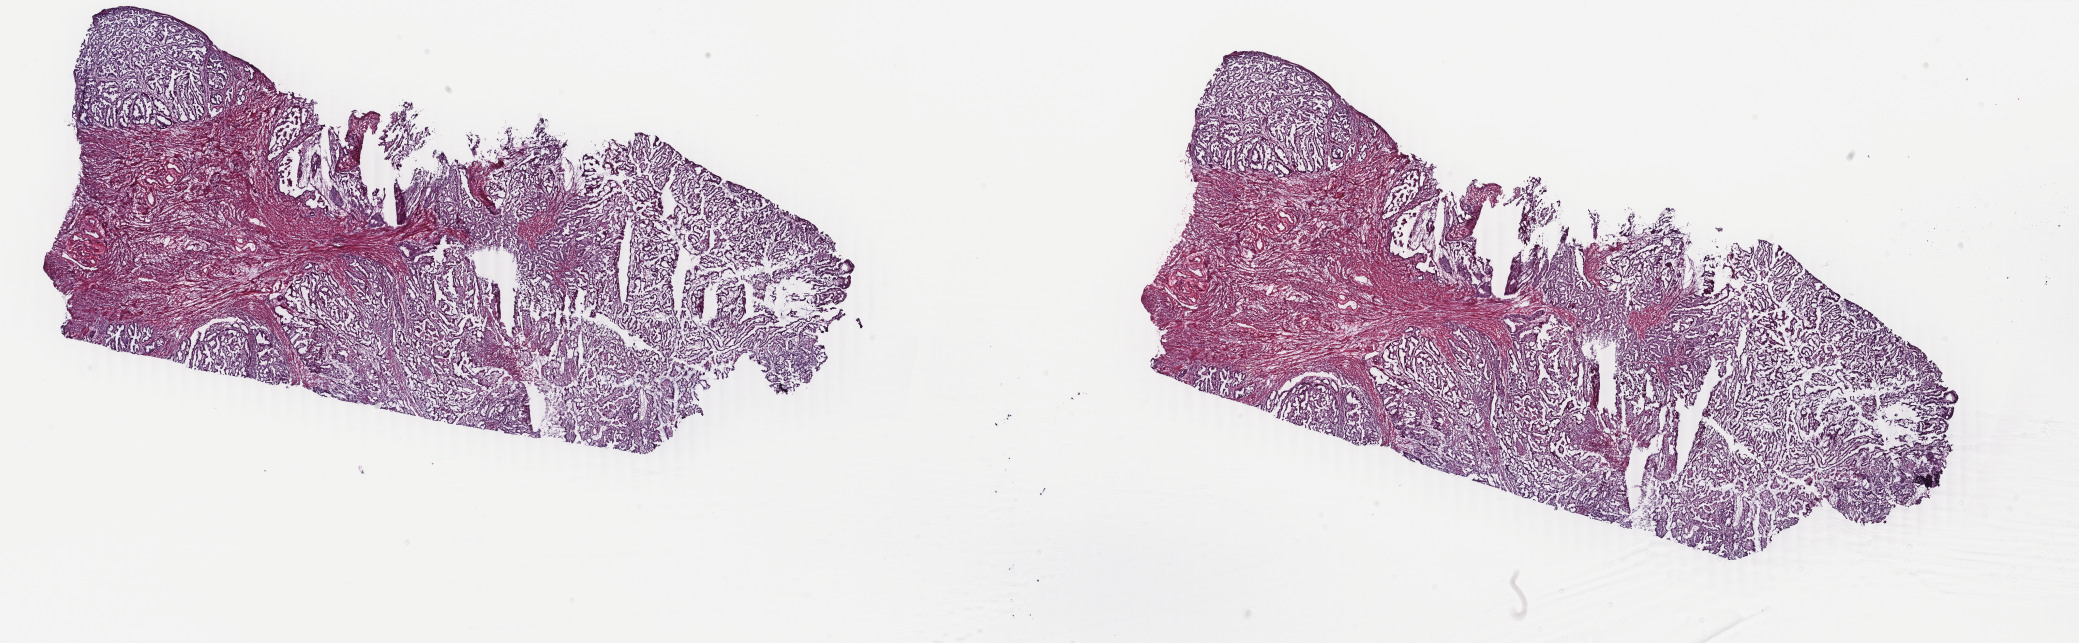
Digitized H&E-stained tissue section (whole slide), a low-resolution overview of the entire scanned area, about 33.1 x 10.2 mm (from a 40x scan), frozen section, sample: primary tumour, uterus. Patient: female, age at initial diagnosis 60 years. Histologic grade: G2 (moderately differentiated). Slide review estimates, as recorded: tumour cells 66%, tumour nuclei 66%, normal cells 0%, stromal cells 34%, necrosis 0%. Inflammatory infiltration, as recorded: lymphocyte infiltration 0%, monocyte infiltration 0%, neutrophil infiltration 0%.
* FIGO stage: IB
* pathologic diagnosis: Endometrioid adenocarcinoma, NOS (endometrium)